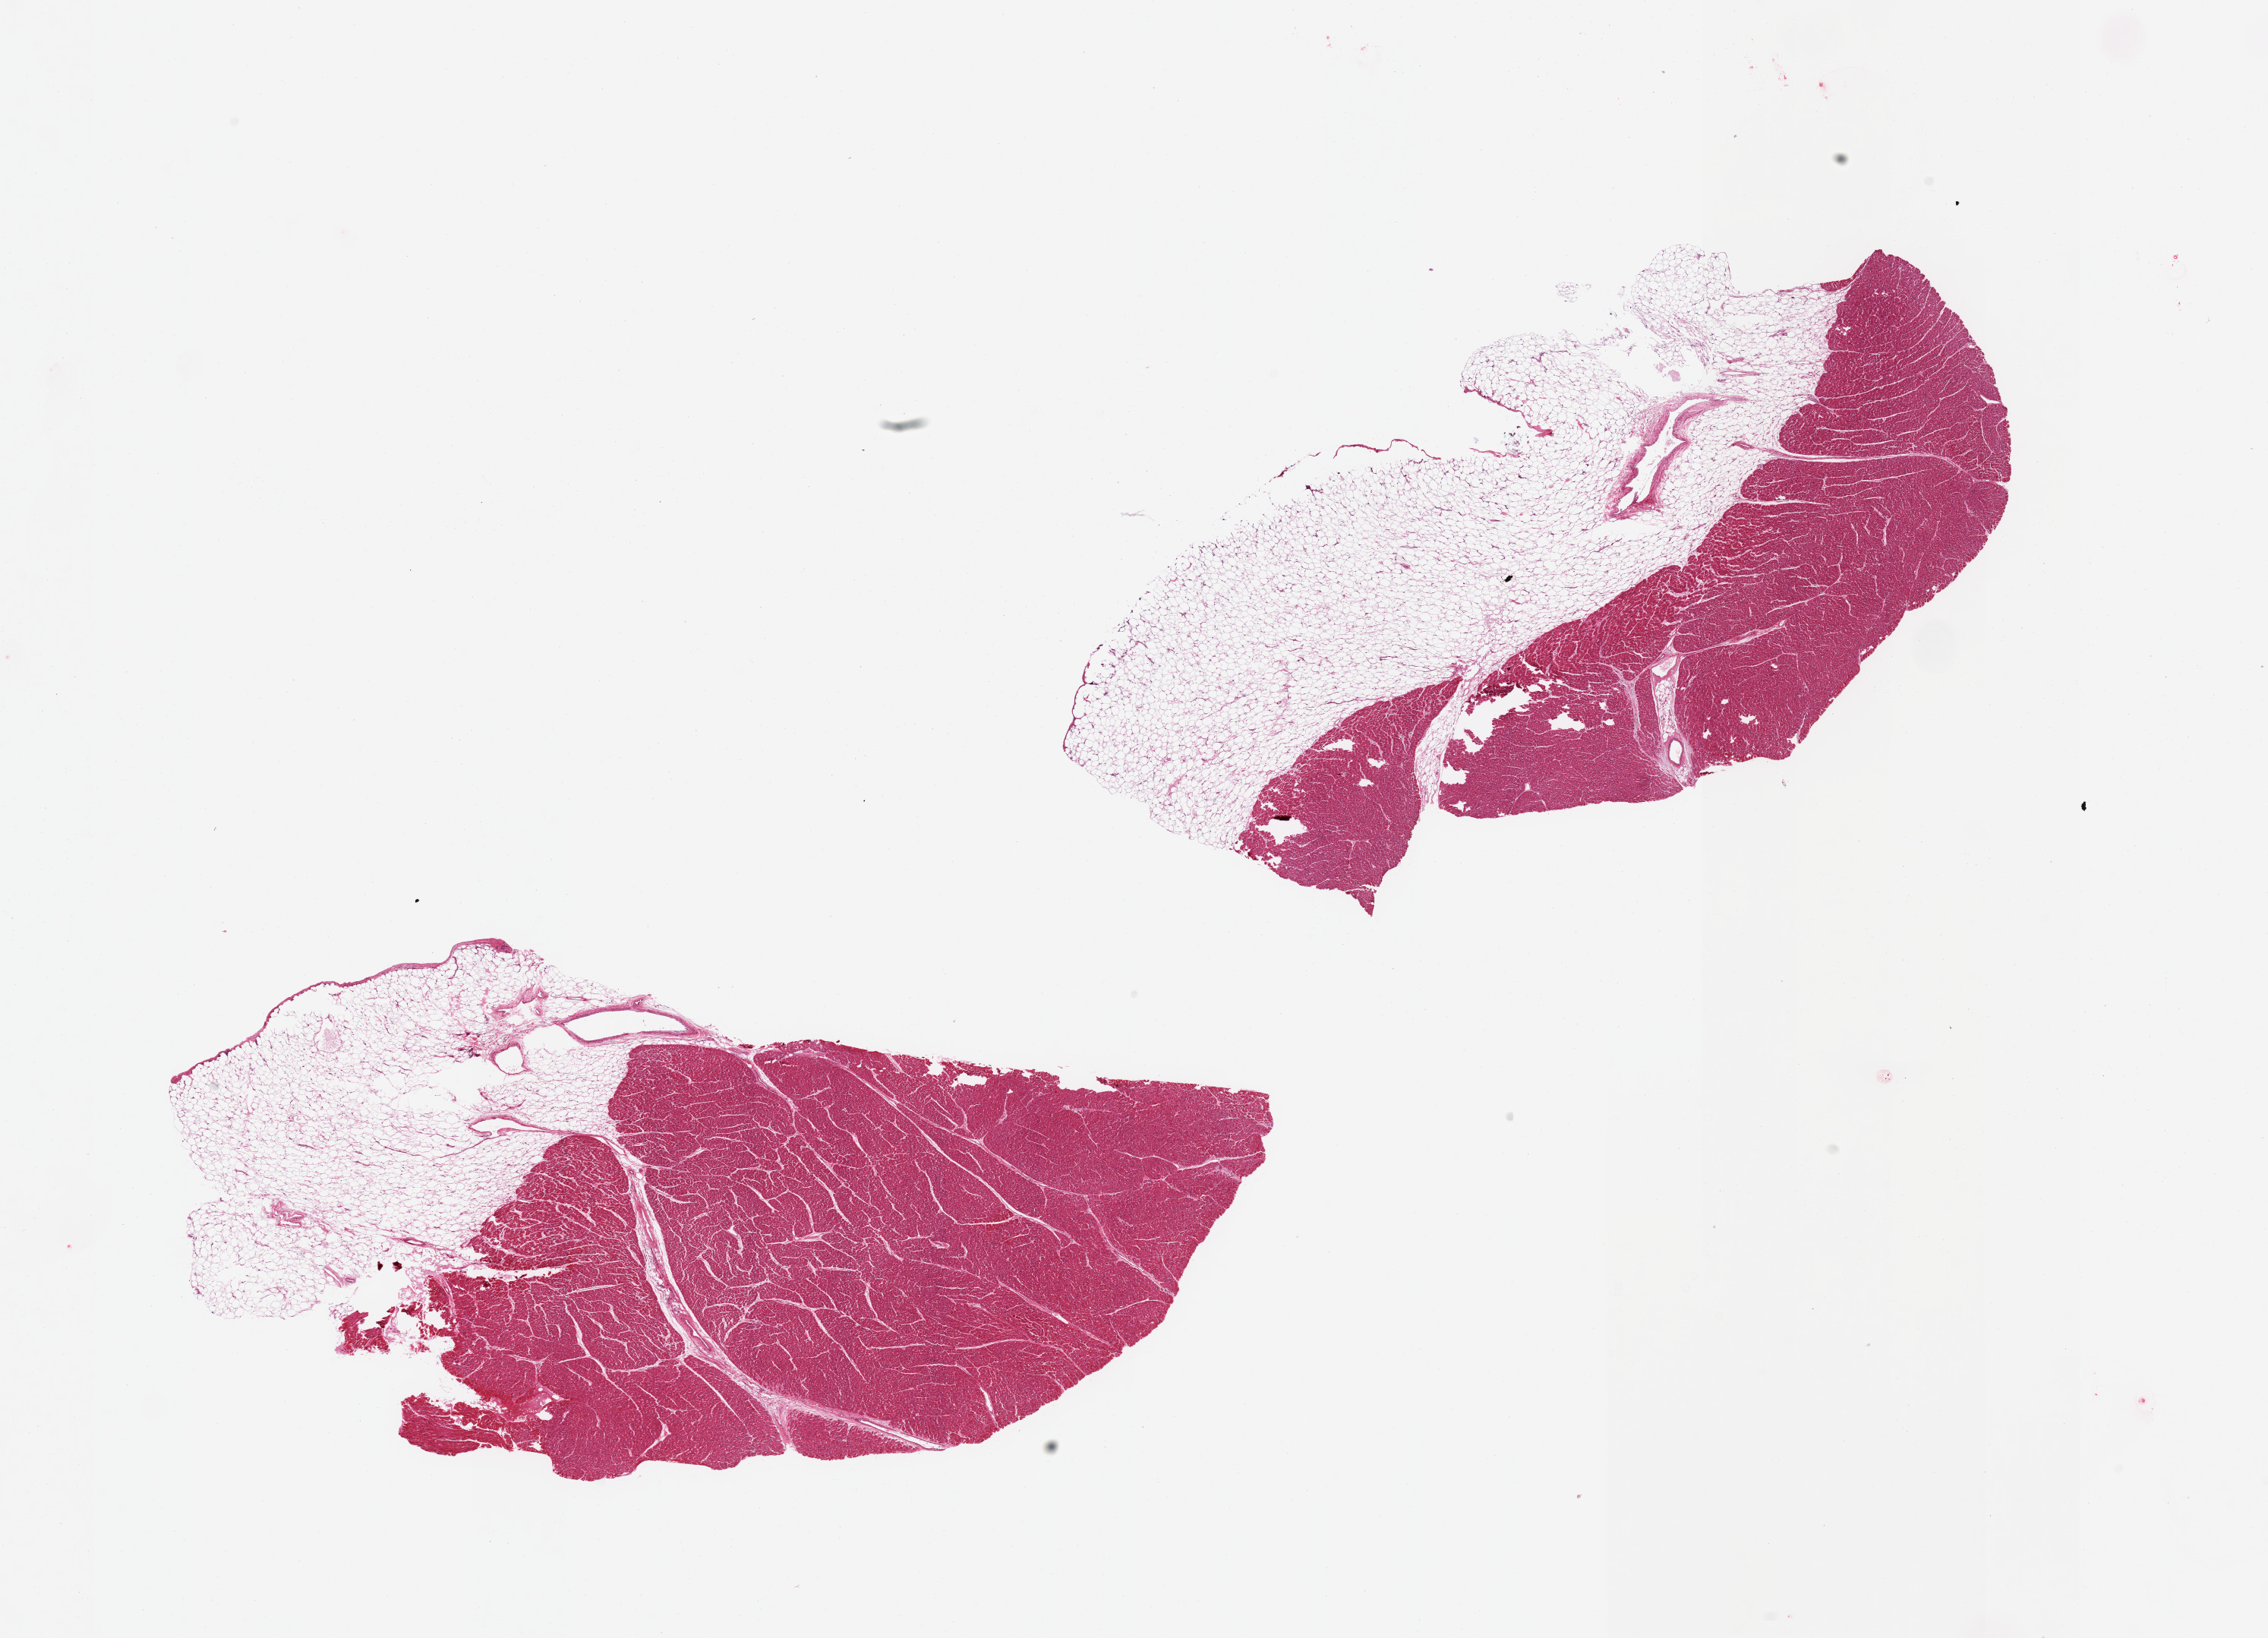
Digitized hematoxylin and eosin (H&E)-stained section — a low-resolution overview of the entire scanned area, about 23.6 x 17.1 mm (from a 20x scan); PAXgene-fixed, paraffin-embedded tissue; target tissue: coronary artery; tissue donor sample. Donor sex: male.
Pathologist's review note for this sample: 2 pieces; myocardium; 40% and 50% external fat attached; coronary artery not identified.